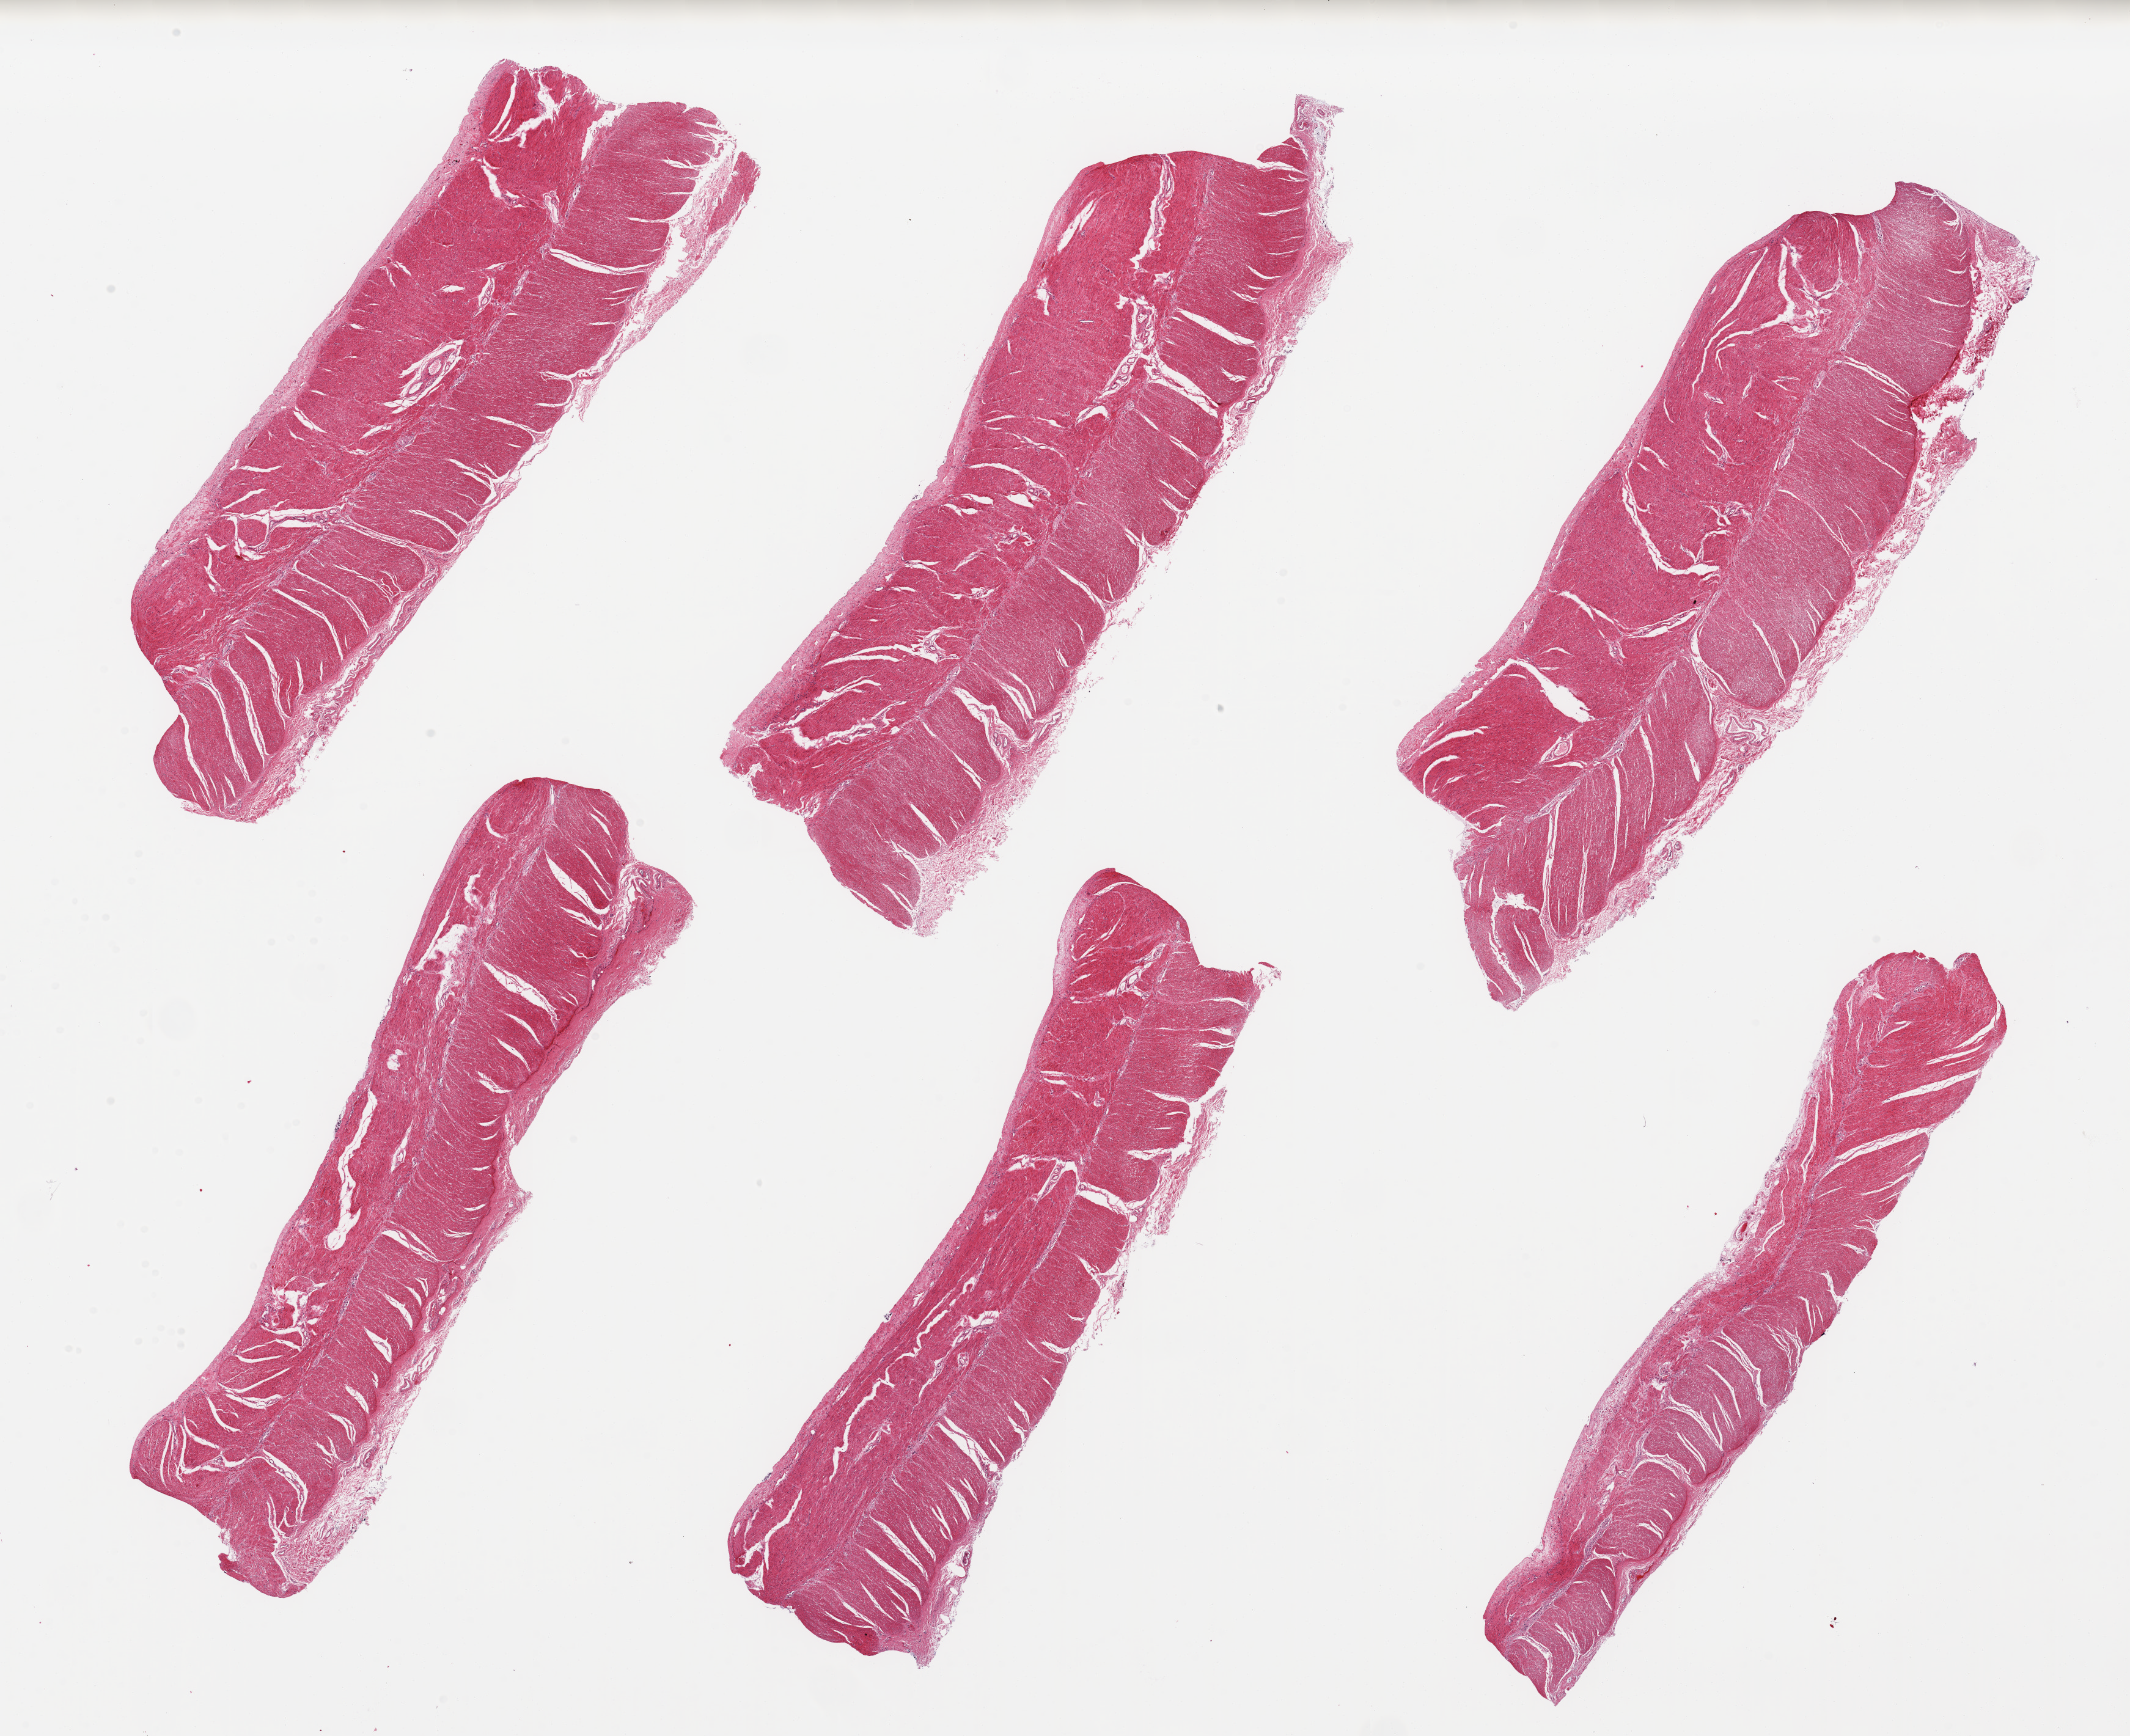
Whole-slide image, hematoxylin and eosin (H&E) stain, shown as a low-resolution overview of the whole scanned area (about 27.6 x 22.5 mm, from a 20x scan); PAXgene-fixed paraffin-embedded (PFPE) section; section of sigmoid colon (target tissue); donor tissue sample. Donor: male.
Review note (as recorded): 6 pieces; target muscularis and attached rim of serosa.